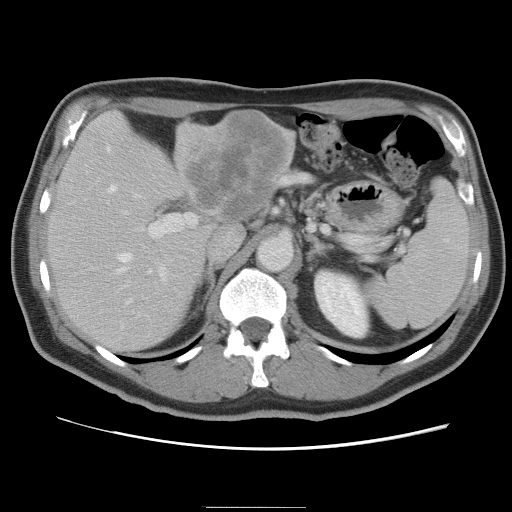
Contrast-enhanced abdominal CT, one axial slice. Slice 51 of 87 in the series (ordered by position). 120 kVp. Intravenous contrast given. Soft-tissue window (W 400 / L 40 HU). 5 mm slice thickness. 512 × 512 image matrix, field of view 363 × 363 mm. Male patient, age 63 years. Case-level facts recorded for this patient, not image findings: diagnosis: colorectal cancer liver metastases, imaged before liver resection; multiple liver metastases: no; largest metastasis: 9 cm; disease in both lobes: no.
Annotated regions visible in this slice (expert manual segmentation):
- hepatic veins: bounding box (x1, y1, x2, y2) in pixels: (106, 147, 152, 304)
- liver: (48, 112, 296, 355)
- planned liver remnant (the part of the liver to remain after resection): (49, 146, 205, 355)
- portal vein (with intrahepatic branches): (96, 182, 198, 315)
- liver metastasis: (187, 117, 285, 222)